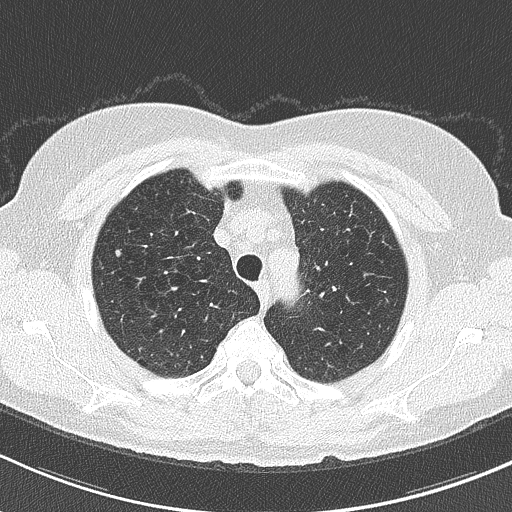
Chest CT (low-dose screening protocol), one axial image. First (baseline) screen. Lung window (W 1500 / L -600 HU). 2 mm slice thickness. Slice 36 of 202 in the series. 512 × 512 image matrix. Female participant, aged 60 years at enrolment. Former smoker at enrolment.
Expert-annotated lung lesion, bounding box [x1, y1, x2, y2] px = [105, 240, 132, 269]. Reader record for this screening exam (exam-level; its link to the box is not recorded): non-calcified nodule or mass ≥4 mm, right upper lobe, 4 × 4 mm, smooth margins, soft tissue attenuation. Official screen result: positive, change unspecified: nodule(s) >= 4 mm or enlarging nodule(s), mass(es), or other non-specific abnormalities suspicious for lung cancer. Later outcome: lung cancer diagnosed 216 days after this screen — acinar cell carcinoma, right upper lobe, well differentiated (G1), stage IA (AJCC 6th edition), 7 mm at pathology.